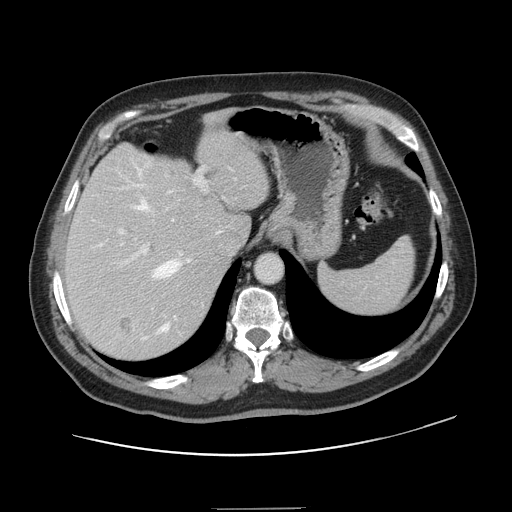
Contrast-enhanced abdominal CT, one axial slice; position 107 of 143 along the scan axis; 120 kVp; intravenous contrast given; soft-tissue window (W 400 / L 40 HU); 2.5 mm slice thickness; 512 × 512 image matrix, field of view 402 × 402 mm. Male patient, age 62 years. From the clinical record (not read from this slice): diagnosis: colorectal cancer liver metastases, imaged before liver resection; multiple liver metastases: yes; largest metastasis: 2.7 cm; disease in both lobes: no.
Structures marked on this image (outlined manually by an expert reader):
- hepatic veins: box from (x=100, y=167) to (x=190, y=339) px
- liver: (x=66, y=121)–(x=269, y=359)
- planned liver remnant (the part of the liver to remain after resection): (x=66, y=123)–(x=269, y=272)
- portal vein (with intrahepatic branches): (x=119, y=167)–(x=205, y=276)
- liver metastasis: (x=117, y=316)–(x=135, y=335)
- liver metastasis: (x=167, y=163)–(x=181, y=180)